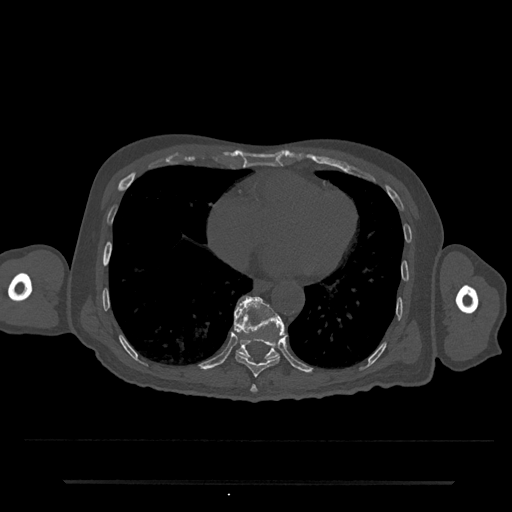
CT including the spine, one axial slice. Position 347 of 797 along the scan axis. Reconstruction kernel Br40s/3. 120 kVp. Bone window (W 1800 / L 400 HU). 0.5 mm slice thickness. 512 × 512 image matrix, field of view 427 × 427 mm. Patient: male, 74 years. From the clinical record (not read from this slice): primary cancer: prostate.
Annotated regions visible in this slice (semi-automatically segmented with operator editing):
- T10 vertebra: box from (x=234, y=296) to (x=285, y=361) px
- T8 vertebra: (x=250, y=385)–(x=258, y=393)
- T9 vertebra: (x=234, y=296)–(x=285, y=377)